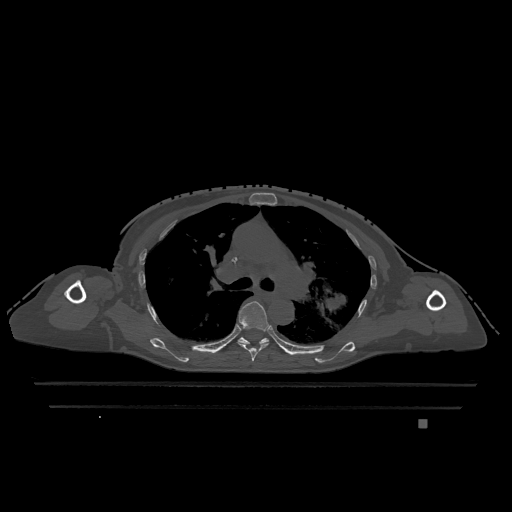
CT including the spine, one axial slice. Position 818 of 1317 along the scan axis. Bone window (W 1800 / L 400 HU). 512 × 512 image matrix, field of view 500 × 500 mm. Female patient, age 74 years. From the clinical record (not read from this slice): primary cancer: lung; vertebrae with lytic lesions (as recorded): T1, T4, T5, T6, L4, L5.
Structures marked on this image (semi-automatically segmented with operator editing):
- T5 vertebra: bounding box [x1, y1, x2, y2] px = [238, 301, 269, 361]
- T6 vertebra: [238, 337, 269, 344]